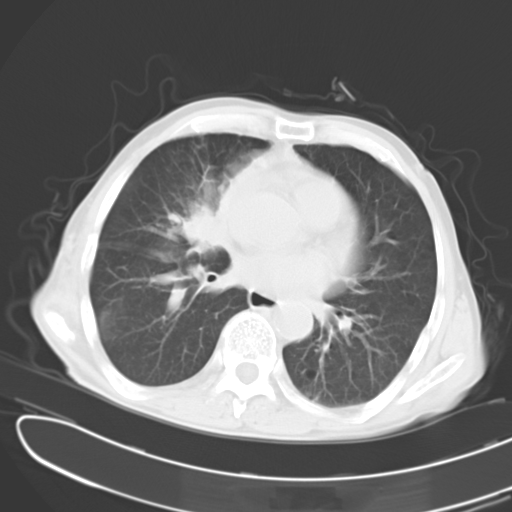
Chest CT, one axial slice. Slice 9 of 24 in the series (ordered by position). Reconstruction kernel B40f. 120 kVp. Lung window (W 1500 / L -600 HU). 10 mm slice thickness. 512 × 512 image matrix, field of view 353 × 353 mm. Patient: male, 65 years. From the clinical record (not read from this slice): clinical TNM (as recorded): T2 N3 M1; histopathological grade: G3.
Annotated regions visible in this slice (bounding box drawn by a radiologist):
- lung tumour (recorded histology: small cell carcinoma): box from (x=174, y=192) to (x=225, y=257) px